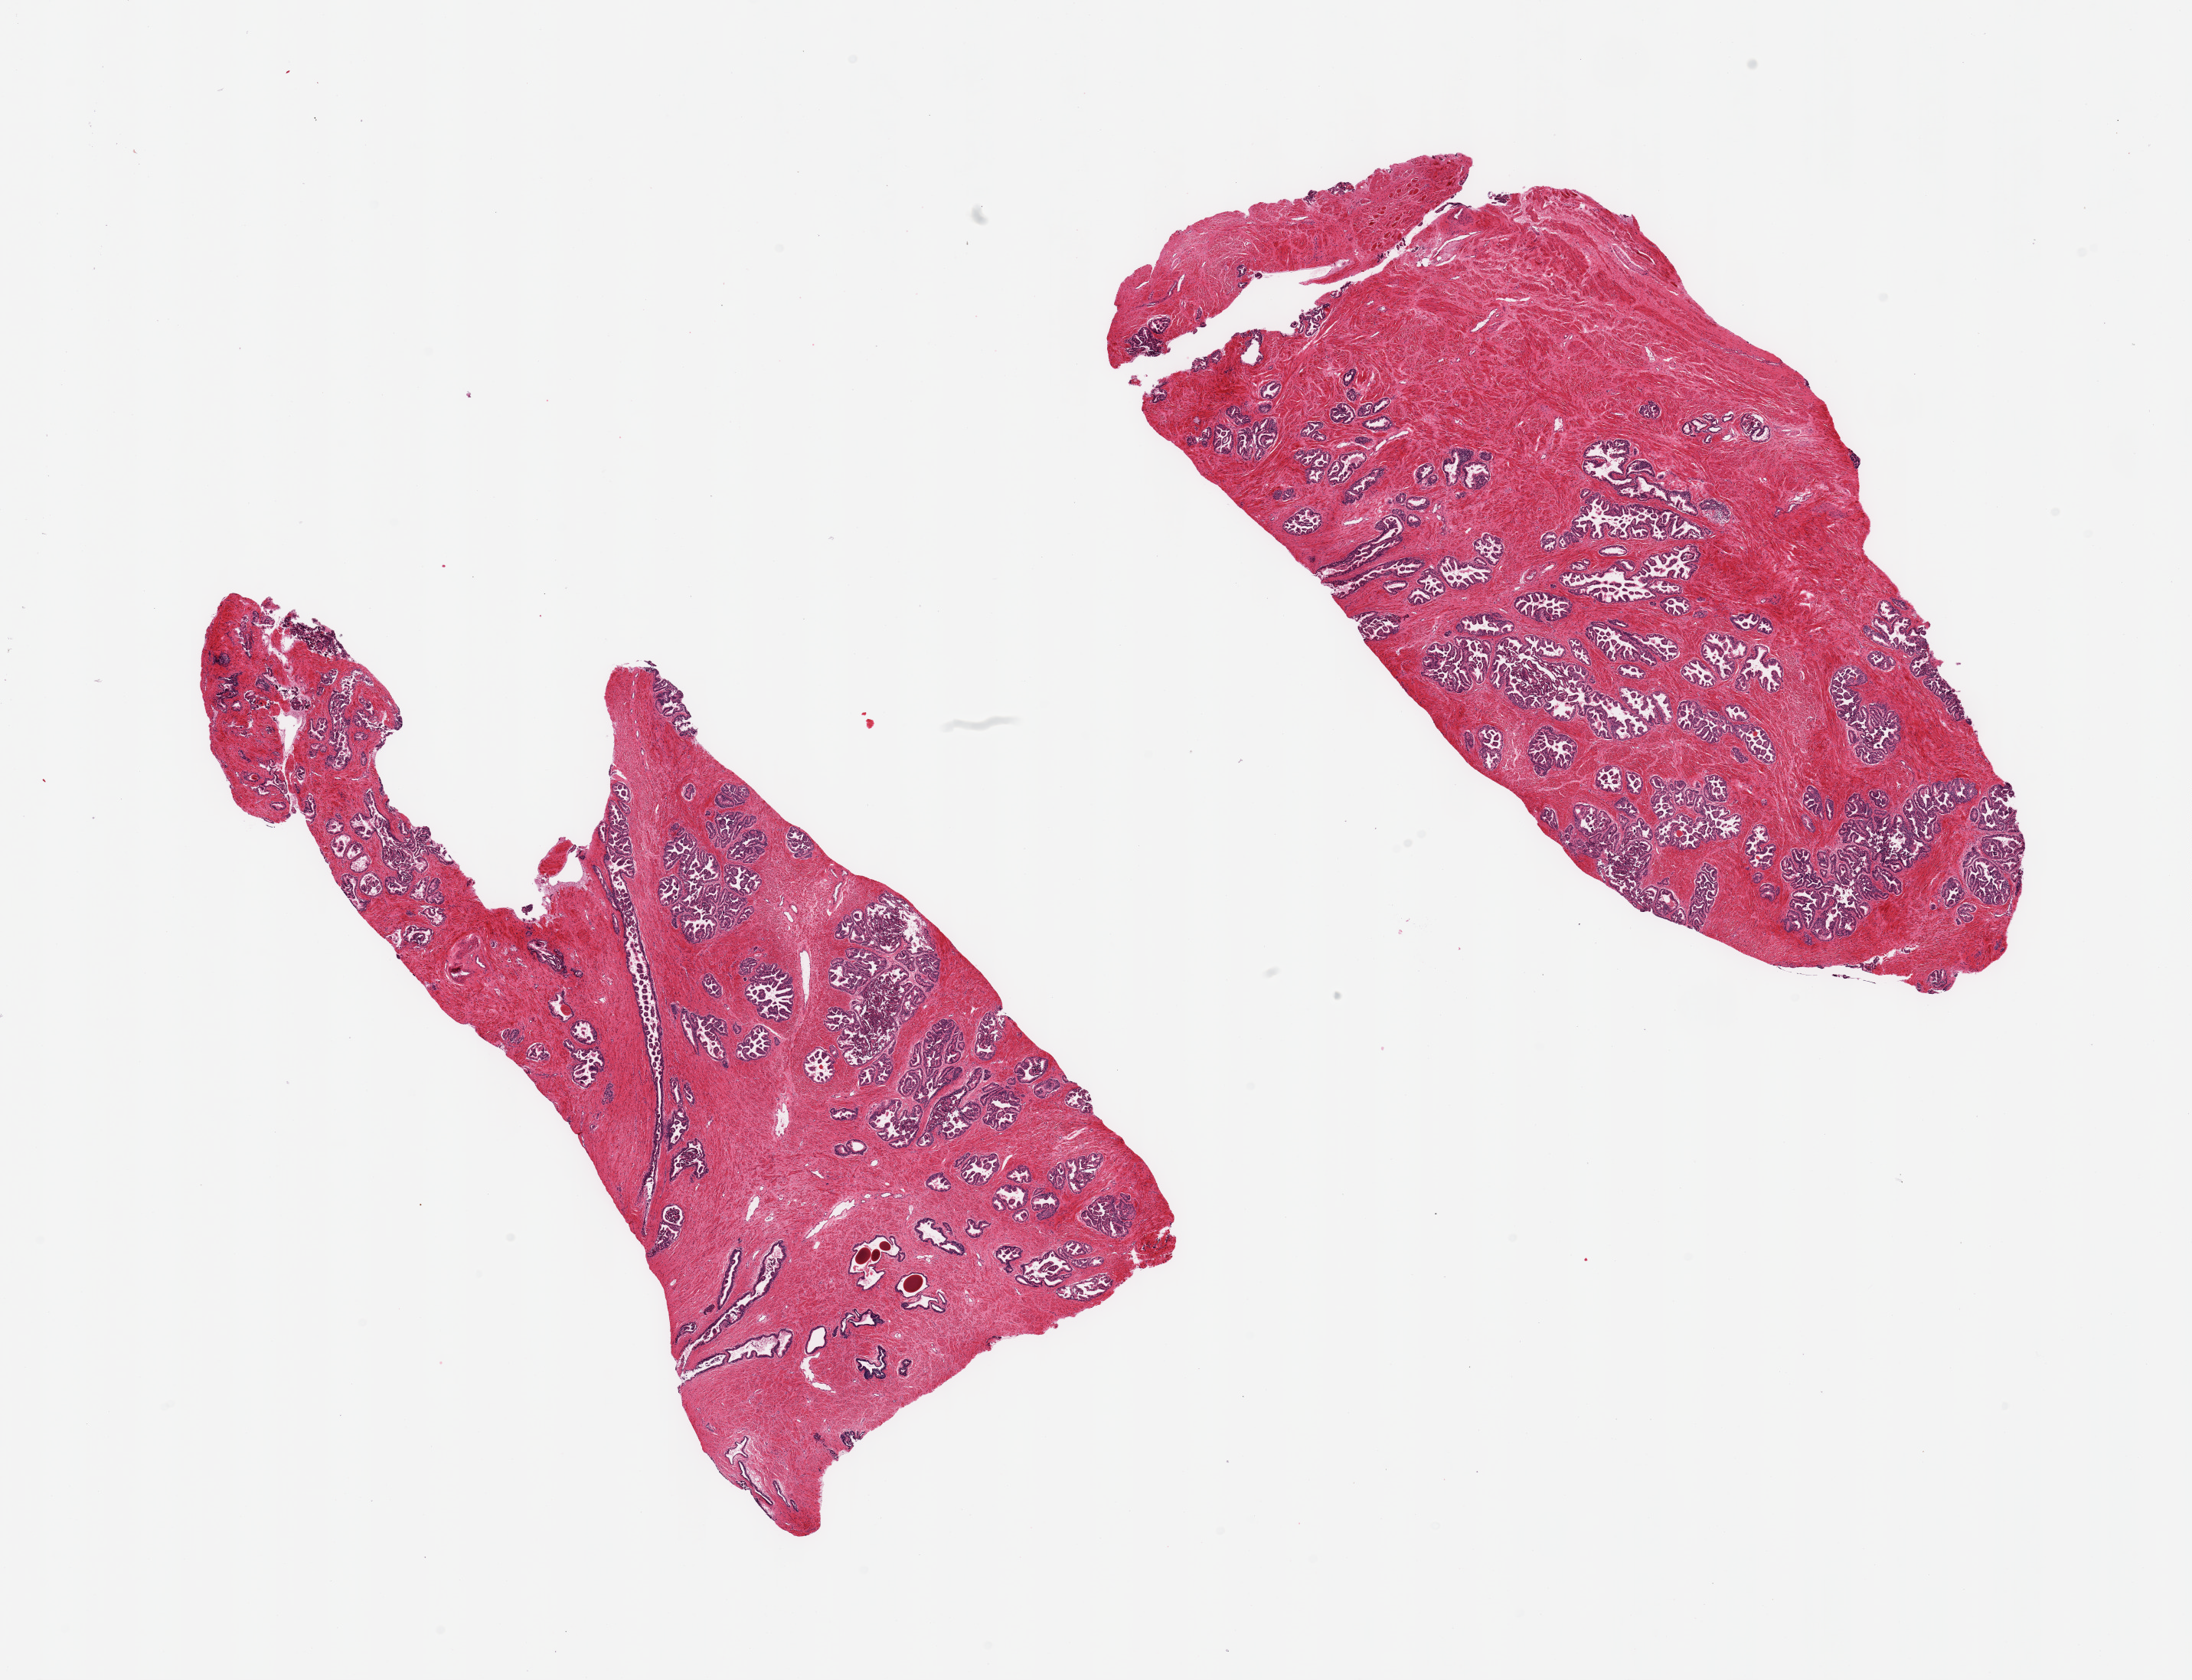
H&E whole-slide image, brightfield — shown as a low-resolution overview of the whole scanned area (about 22.6 x 17.4 mm, slide scanned at 20x). PAXgene-fixed paraffin-embedded (PFPE) section. Section of prostate (target tissue). Tissue donor sample.
Pathologist's review note for this sample: 2 pieces; well preserved; no lesions.